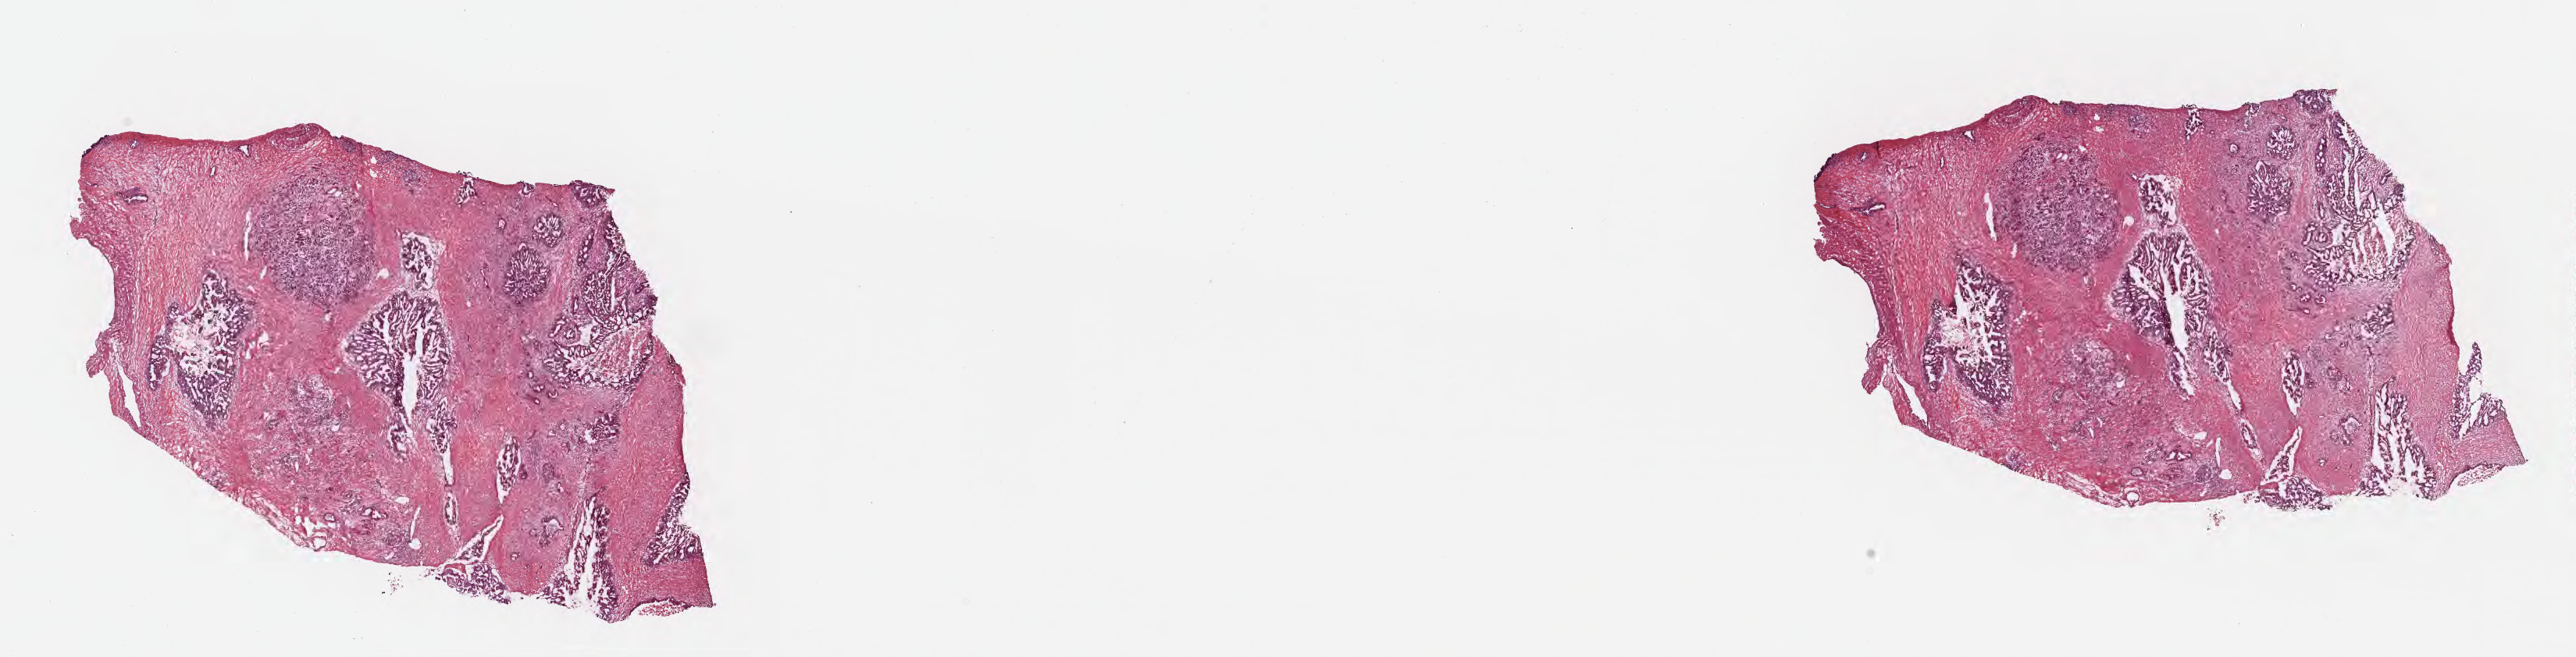
Whole-slide image, hematoxylin and eosin (H&E) stain, a low-resolution overview of the entire scanned area, about 26.7 x 6.8 mm, frozen section (tissue freezing medium), specimen: primary tumor, site: body of pancreas. Male patient; age at initial diagnosis 66 years. Tumor grade: G2 (moderately differentiated). Pathologist review of this section (percent, as recorded): tumor cells 60%, tumor nuclei 60%, stromal cells 16%, necrosis 4%, normal cells 20%. Inflammatory infiltration, as recorded: lymphocyte infiltration 8%, monocyte infiltration 1%, neutrophil infiltration 5%.
• AJCC pathologic stage: Stage III
• diagnosis: Infiltrating duct carcinoma, NOS
• section: top of the tissue portion